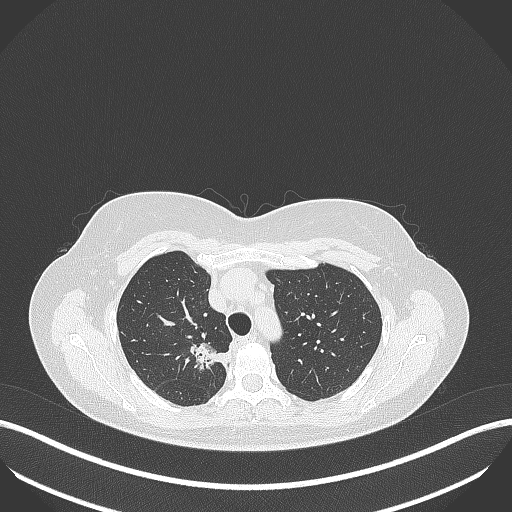
Chest CT, one axial slice; slice 300 of 386 in the series (ordered by position); reconstruction kernel B70f; lung window (W 1500 / L -600 HU); 1 mm slice thickness; 512 × 512 image matrix, field of view 400 × 400 mm. Patient: female, 65 years. From the clinical record (not read from this slice): clinical TNM (as recorded): T1b N0 M0.
Structures marked on this image (bounding box drawn by a radiologist):
- lung tumour (recorded histology: adenocarcinoma): box from (x=184, y=338) to (x=231, y=373) px